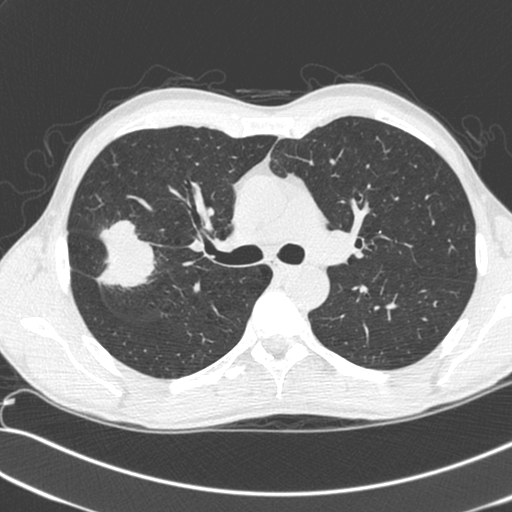
Axial slice from a low-dose chest CT screening exam; baseline annual screen; lung window (W 1500 / L -600 HU); 1.3 mm slice thickness; 120 kVp; slice 90 of 281 in the series. Male participant, aged 55 years at enrolment. Current smoker at enrolment.
Expert-annotated lung lesion, bounding box (x1, y1, x2, y2) in pixels: (67, 221, 156, 298). The exam's reader record, not a measurement of the box and not confirmed to be the same lesion: non-calcified nodule or mass ≥4 mm, right upper lobe, 52 × 39 mm, spiculated (stellate) margins, soft tissue attenuation. Lung cancer was diagnosed 25 days after this screen: large cell neuroendocrine carcinoma, right upper lobe, poorly differentiated (G3), stage IIB (AJCC 6th edition), 49 mm at pathology.